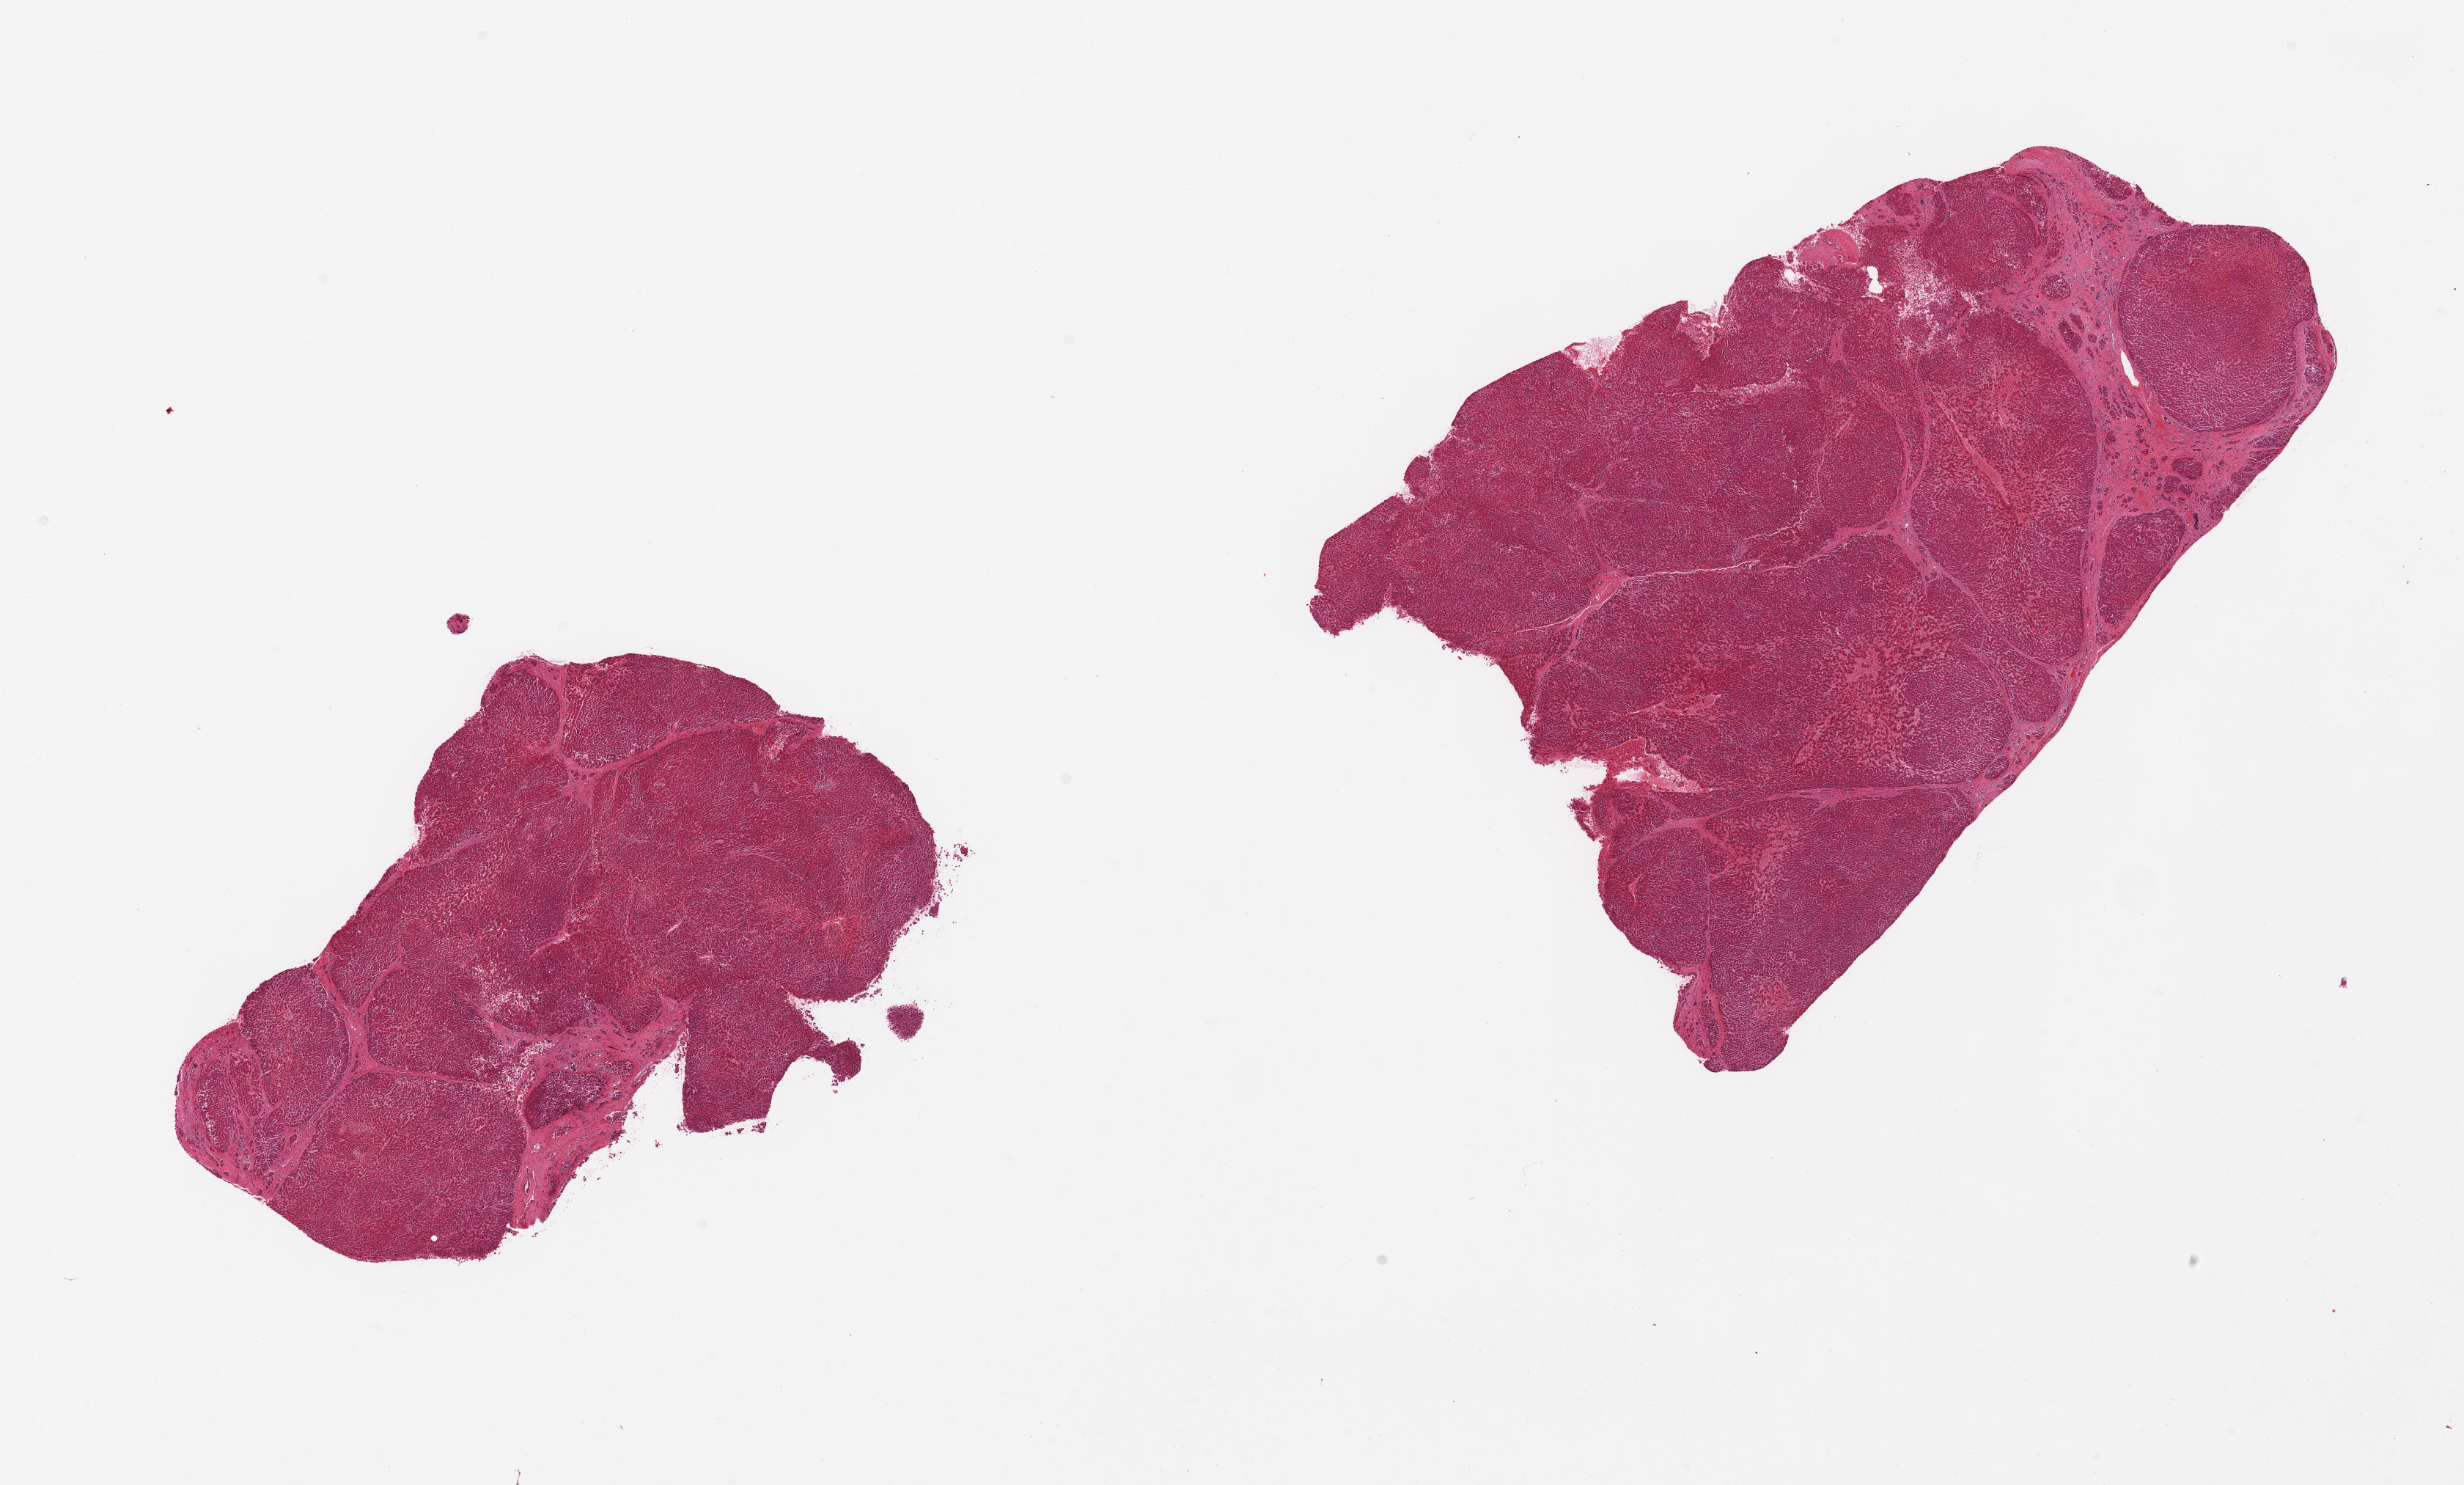
H&E whole-slide image, shown as a low-resolution overview of the whole scanned area (about 26.6 x 16.0 mm); PAXgene-fixed, paraffin-embedded tissue; section of liver (target tissue); tissue donor sample.
* reviewer comment on this tissue sample: 2 pieces, established macronodular cirrhosis